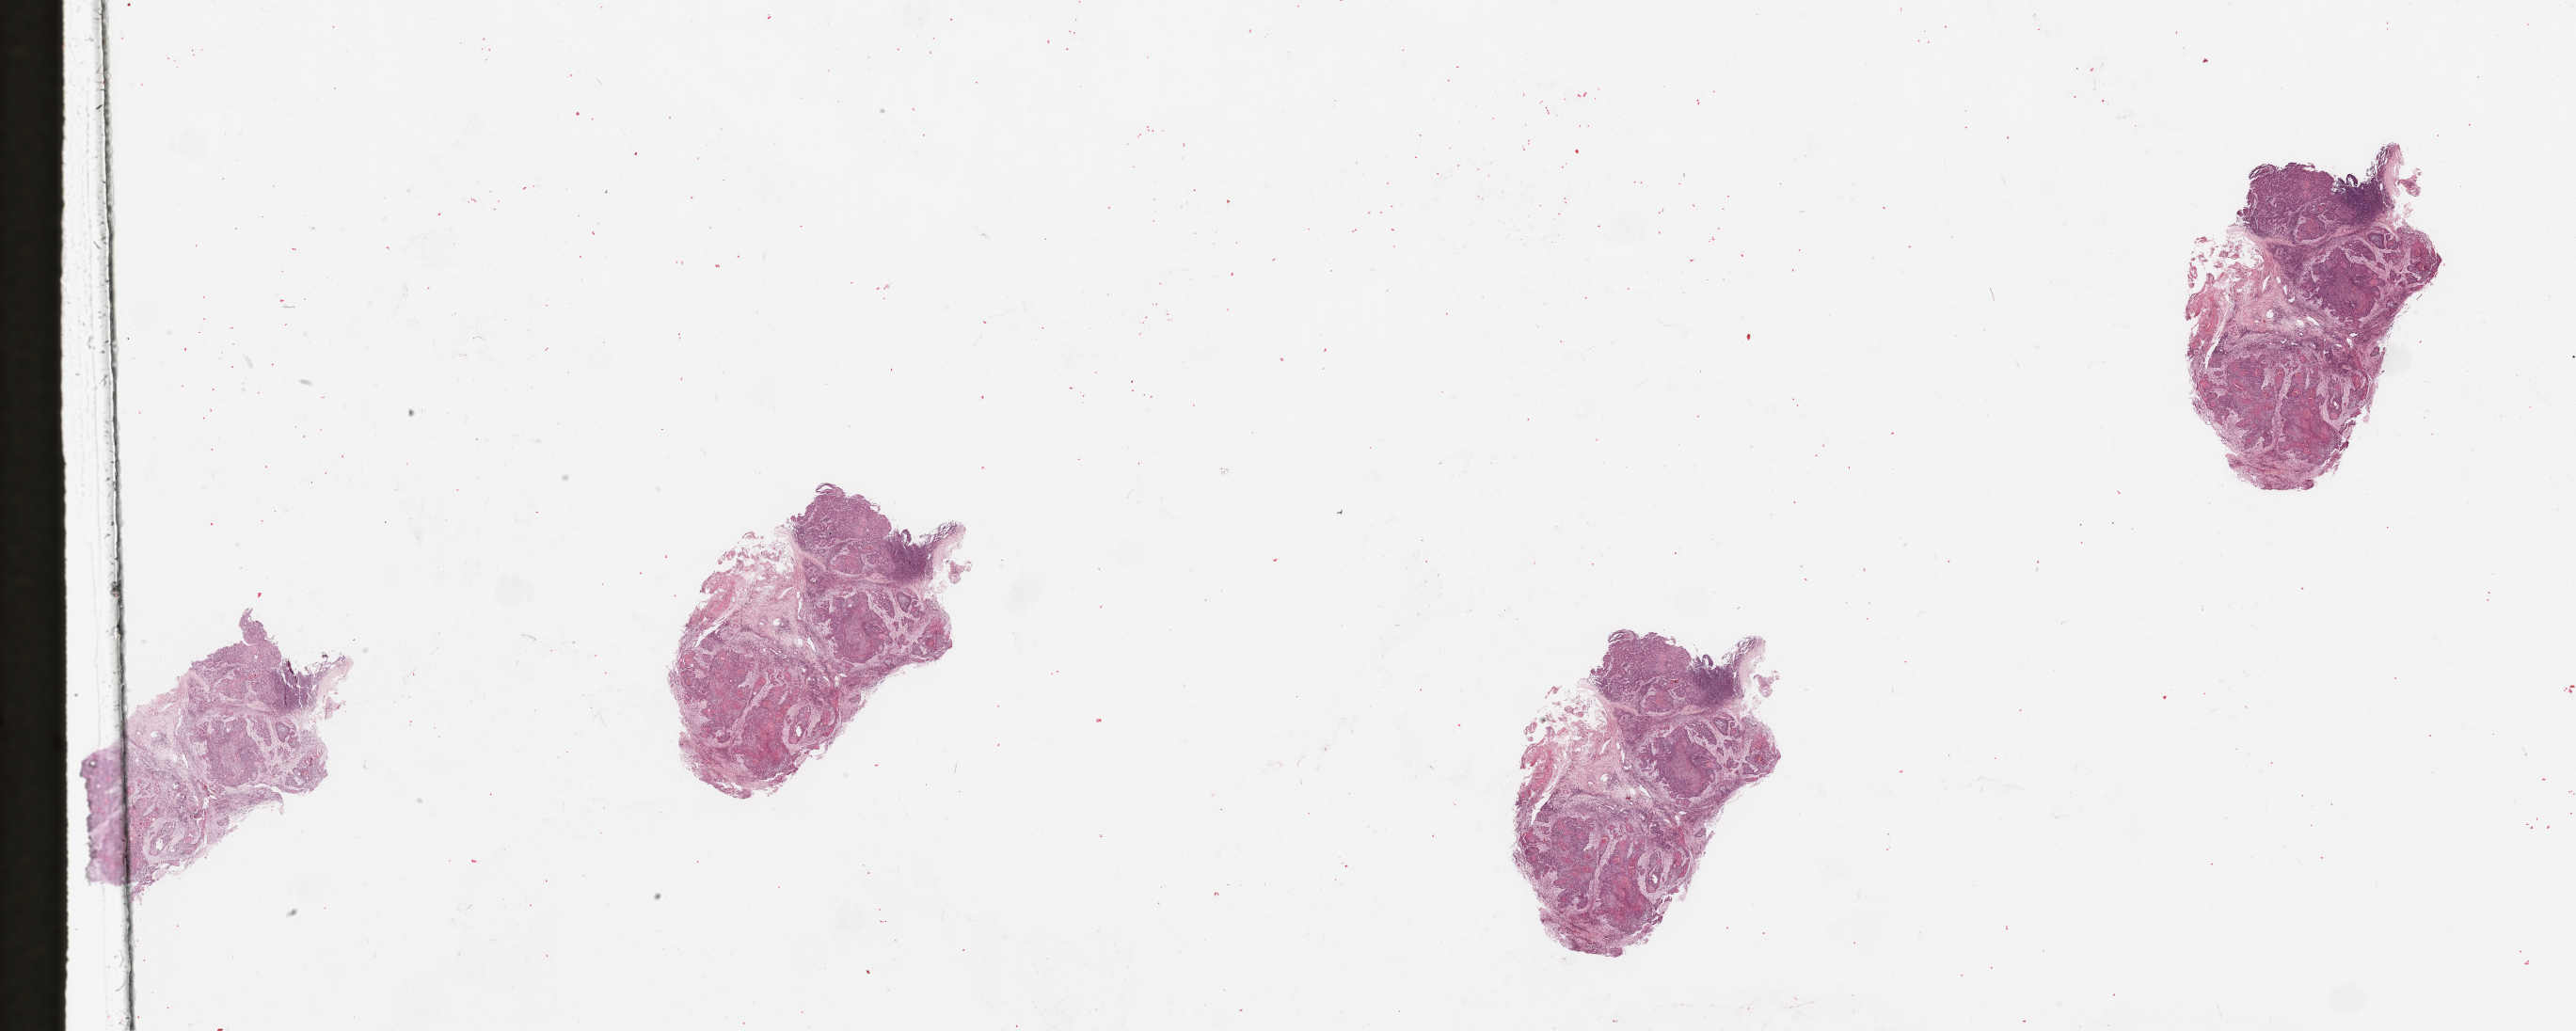
Hematoxylin and eosin (H&E) stained whole-slide image — low-resolution overview of the scanned area, about 43.3 x 17.3 mm (from a 20x scan). Tumour tissue sample, sampled site: alveolar ridge. 67-year-old male patient. Histologic grade: G1 (well differentiated). Slide review estimates, as recorded: tumour nuclei 80%, necrosis 5%.
• primary tumour site (as recorded): oral cavity
• AJCC pathologic stage: IVA
• diagnosis: Squamous cell carcinoma, NOS (gum, NOS)